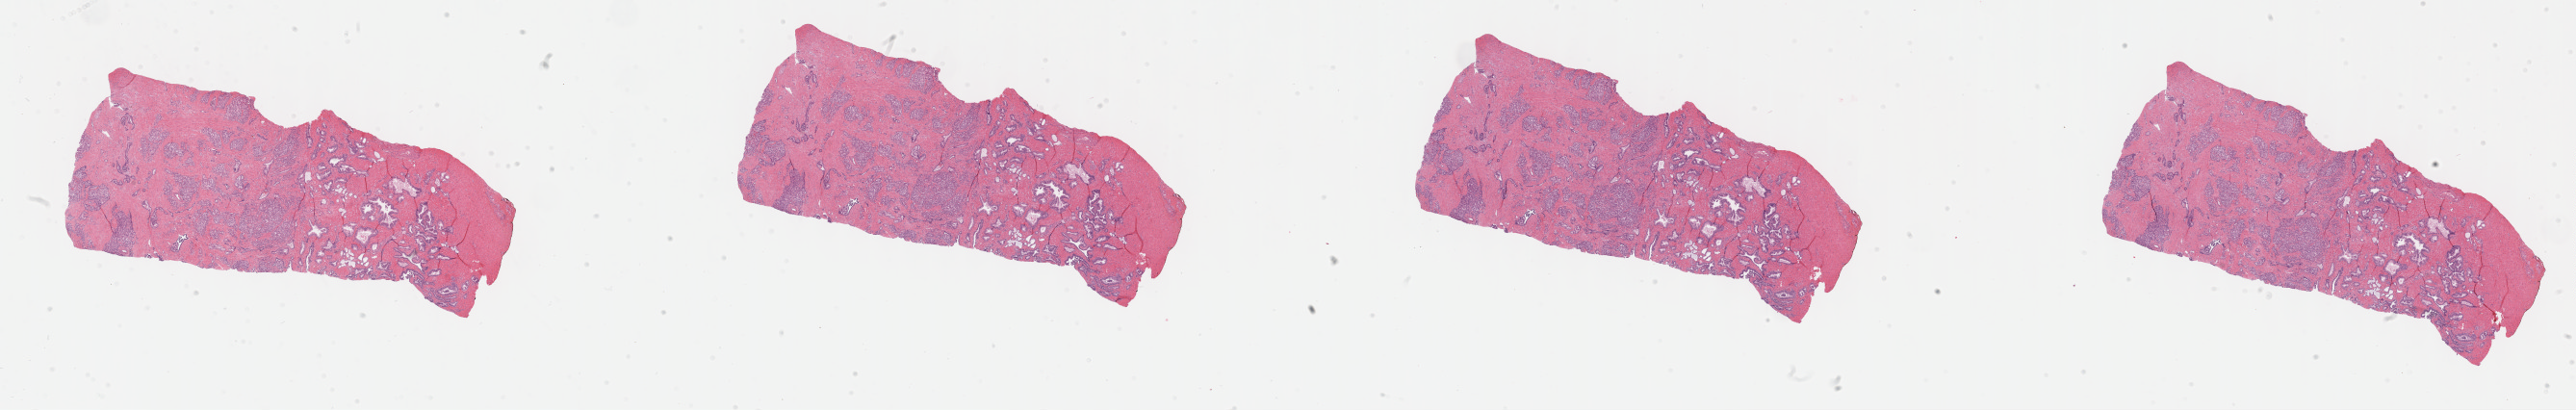
Whole-slide histology image, H&E — a low-resolution overview of the entire scanned area, about 43.3 x 6.9 mm, formalin-fixed paraffin-embedded (FFPE) diagnostic section, primary tumour sample from the prostate. Male patient; age at initial diagnosis 61 years. Gleason score: 7 (4+3). Slide review estimates, as recorded: tumour cells 25%, tumour nuclei 75%, normal cells 18%, stromal cells 55%, necrosis 2%. Infiltration values recorded for this section: lymphocyte infiltration 3%, monocyte infiltration 0%, neutrophil infiltration 0%.
Lymph nodes positive (case pathology): 0 of 8 examined. Laterality: bilateral. Pathologic diagnosis: Adenocarcinoma, NOS (prostate gland).